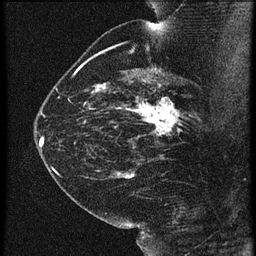
Breast MRI (dynamic contrast-enhanced), one sagittal slice. Position 39 of 60 along the scan axis. 3 images stored at this slice position (order not interpretable as contrast timing). 1.5 T. TE 4.2 ms, TR 21.3 ms. 1.5 mm slice thickness. 256 × 256 image matrix, field of view 180 × 180 mm. Patient: female, 42 years. From the clinical record (not read from this slice): setting: breast cancer imaged before/during neoadjuvant chemotherapy; receptor status: HER2-positive.
Structures marked on this image (semi-automatic segmentation, software-assisted and operator-edited):
- analysis volume of interest (the breast-tissue region the enhancement analysis was run in; not a lesion): bounding box [x1, y1, x2, y2] px = [122, 82, 195, 147]
- tumour enhancement mask (voxels above the 90 % enhancement threshold inside the analysis volume of interest): [125, 82, 186, 135]